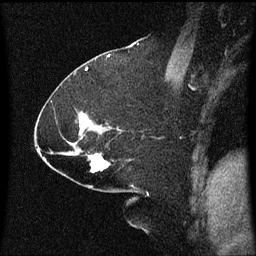
Breast MRI (dynamic contrast-enhanced), one sagittal slice; position 33 of 60 along the scan axis; dynamic contrast-enhanced series, image 2 of 3 at this slice position (ordered by acquisition); 1.5 T; TE 4.2 ms, TR 8 ms; 2.1 mm slice thickness; 256 × 256 image matrix, field of view 200 × 200 mm. Female patient, age 59 years.
Annotated regions visible in this slice (semi-automatically segmented with operator editing):
- analysis volume of interest (the breast-tissue region the enhancement analysis was run in; not a lesion): bounding box [x1, y1, x2, y2] px = [86, 154, 111, 173]
- tumour enhancement mask (voxels above the 70 % enhancement threshold inside the analysis volume of interest): [90, 154, 107, 173]